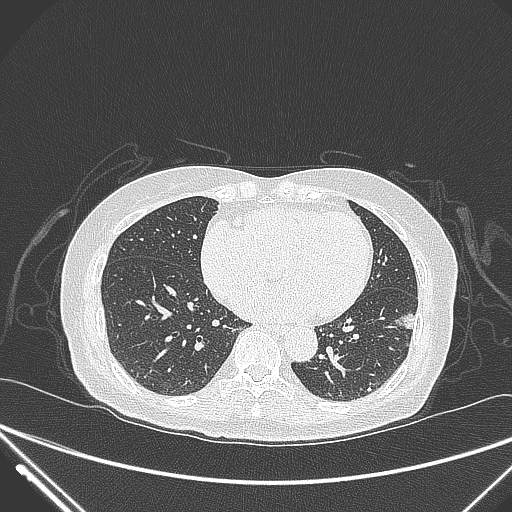
Chest CT, one axial slice; position 115 of 310 along the scan axis; lung window (W 1500 / L -600 HU); 512 × 512 image matrix, field of view 377 × 377 mm. Patient: female, 82 years. Case-level facts recorded for this patient, not image findings: clinical TNM (as recorded): T1c N0 M0.
Structures marked on this image (bounding box drawn by a radiologist):
- lung tumour (recorded histology: adenocarcinoma): bounding box <397,306,421,339> (left, top, right, bottom; pixels)